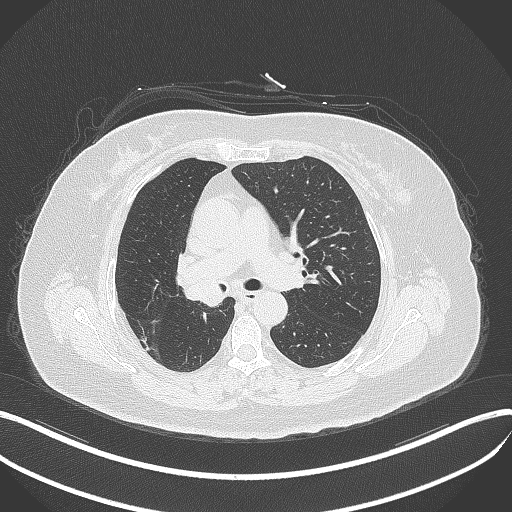
Chest CT, one axial slice. Slice 222 of 376 in the series (ordered by position). Reconstruction kernel B70f. Lung window (W 1500 / L -600 HU). 1 mm slice thickness. 512 × 512 image matrix. Female patient, age 60 years. From the clinical record (not read from this slice): clinical TNM (as recorded): T1c N0 M0.
Structures marked on this image (bounding box drawn by a radiologist):
- lung tumour (recorded histology: squamous cell carcinoma): bounding box (x1, y1, x2, y2) in pixels: (182, 269, 227, 309)